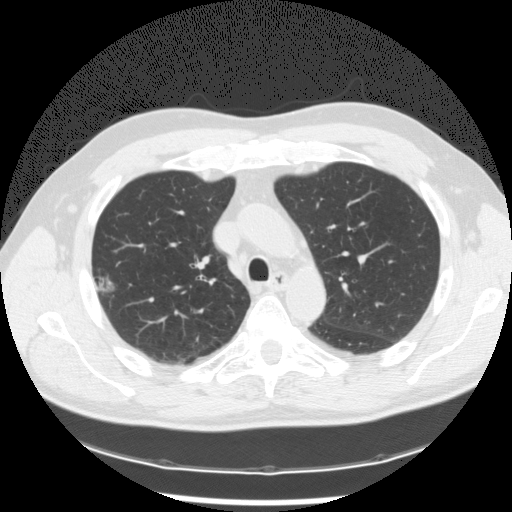
Axial slice from a low-dose chest CT screening exam, baseline annual screen, lung window (W 1500 / L -600 HU), slice 39 of 119 in the series. Male participant, aged 62 years at enrolment. Former smoker at enrolment.
Expert-annotated lung lesion, bounding box <89,269,121,301> (left, top, right, bottom; pixels). The exam's reader record, not a measurement of the box and not confirmed to be the same lesion: non-calcified nodule or mass ≥4 mm, right upper lobe, 14 × 11 mm, poorly defined margins, mixed attenuation. Later outcome: lung cancer diagnosed 343 days after this screen (after the second annual screen) — adenocarcinoma, NOS, right upper lobe, poorly differentiated (G3), stage IIB (AJCC 6th edition), 5 mm at pathology.